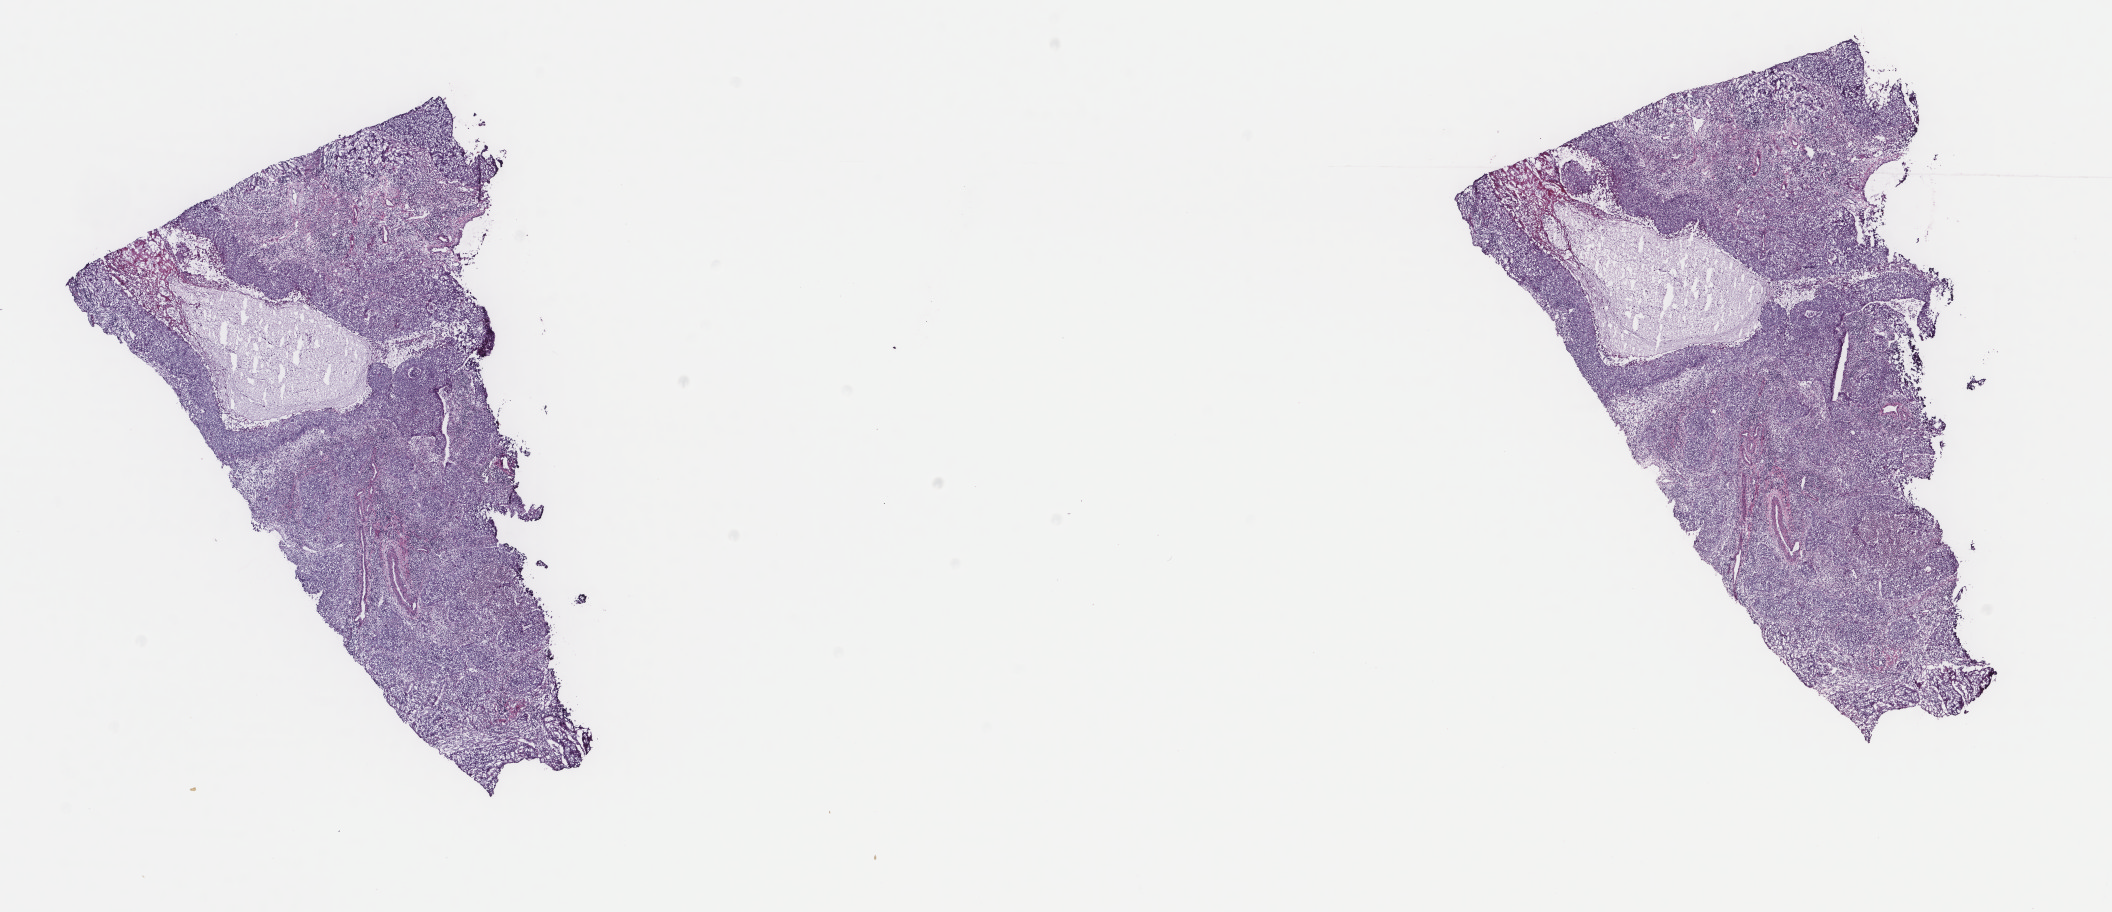
Digitized Hematoxylin and eosin (H&E) stained tissue section (whole slide) — a low-resolution overview of the entire scanned area, about 16.8 x 7.2 mm (from a 40x scan). Frozen section from the top of the tissue portion. Primary tumour sample from the cervix. Female patient; age at initial diagnosis 34 years. Histologic grade: G2 (moderately differentiated). Composition of this section per pathologist review: tumour cells 80%, tumour nuclei 80%, normal cells 0%, stromal cells 20%, necrosis 0%. Infiltration values recorded for this section: lymphocyte infiltration 40%, monocyte infiltration 20%, neutrophil infiltration 20%.
• pathologic diagnosis: Squamous cell carcinoma, NOS
• FIGO stage: IIB